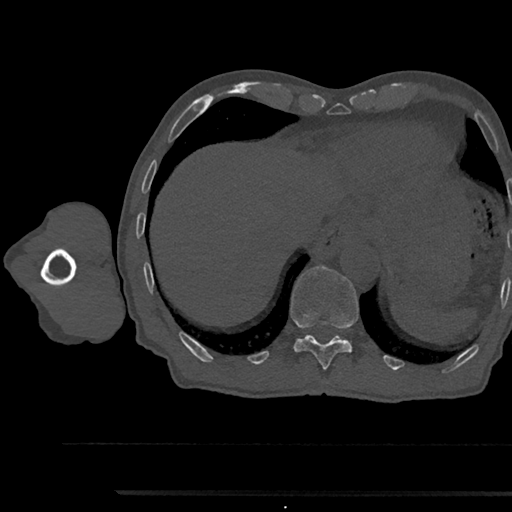
CT including the spine, one axial slice; slice 780 of 797 in the series (ordered by position); reconstruction kernel Br40s/3; 120 kVp; bone window (W 1800 / L 400 HU); 0.5 mm slice thickness; 512 × 512 image matrix, field of view 367 × 367 mm. Patient: male, 79 years. Case-level facts recorded for this patient, not image findings: primary cancer: prostate.
Outlined on this slice (semi-automatic segmentation, software-assisted and operator-edited):
- T11 vertebra: bounding box [x1, y1, x2, y2] px = [290, 266, 359, 370]